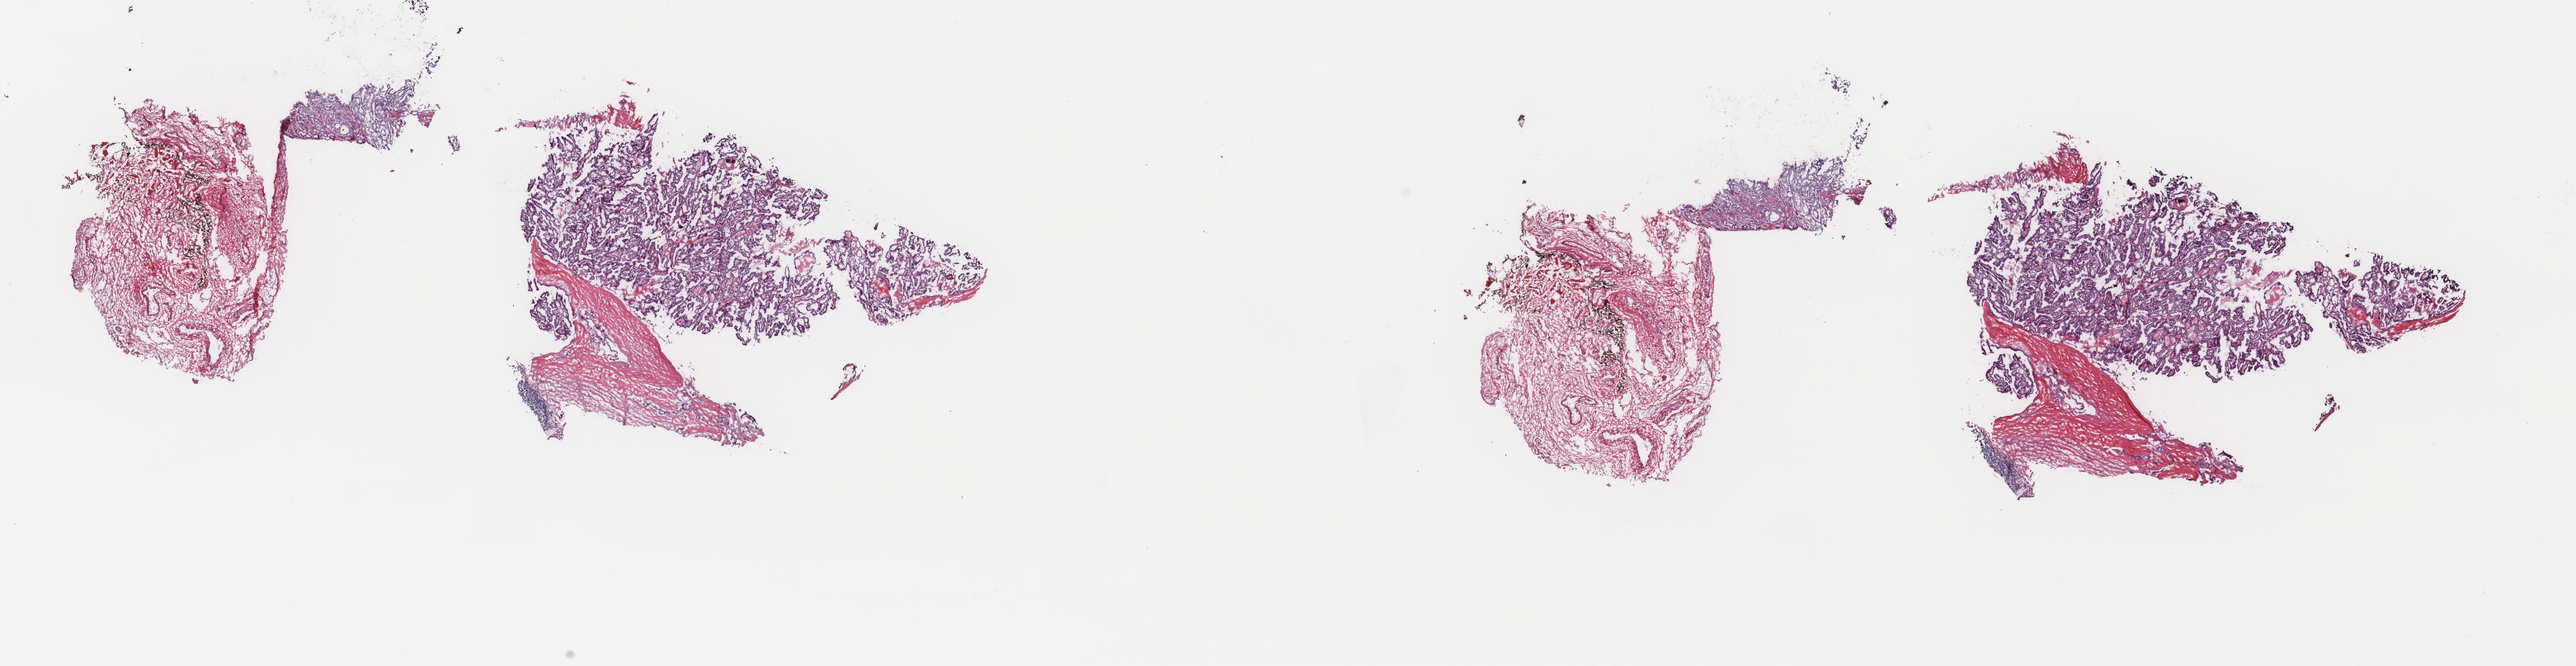
Whole-slide histology image, H&E, a low-resolution overview of the entire scanned area, about 24.8 x 6.4 mm; frozen section from the top of the tissue portion; thyroid, primary tumour sample. Female, age 60 years at initial diagnosis. Slide review estimates, as recorded: tumour cells 80%, tumour nuclei 80%, normal cells 0%, stromal cells 20%, necrosis 0%. Inflammatory infiltration, as recorded: lymphocyte infiltration 5%, monocyte infiltration 1%, neutrophil infiltration 0%.
Diagnosis: Papillary carcinoma, columnar cell (thyroid gland). TNM: T2 N1b MX. AJCC pathologic stage: IVA. Laterality: midline.